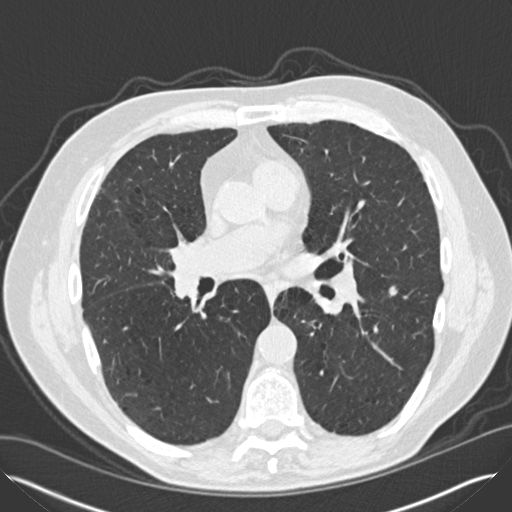
Chest CT (low-dose screening protocol), one axial image. Second screening round (one year after baseline). Lung window (W 1500 / L -600 HU). 2 mm slice thickness. Standard (soft-tissue) reconstruction kernel (B30f). 120 kVp. Male, age 65 years at enrolment.
• Expert-annotated lung lesion, bounding box [x1, y1, x2, y2] px = [372, 276, 413, 312].
• The exam's reader record, not a measurement of the box and not confirmed to be the same lesion: non-calcified nodule or mass ≥4 mm, left lower lobe, 12 × 8 mm, smooth margins, soft tissue attenuation, pre-existing on the prior screen: yes; interval growth: yes.
• Official screen result: positive, other.
• Lung cancer was diagnosed 67 days after this screen: non-small cell carcinoma, left lower lobe, right hilum, poorly differentiated (G3), stage IV (AJCC 6th edition), 5 mm at pathology.